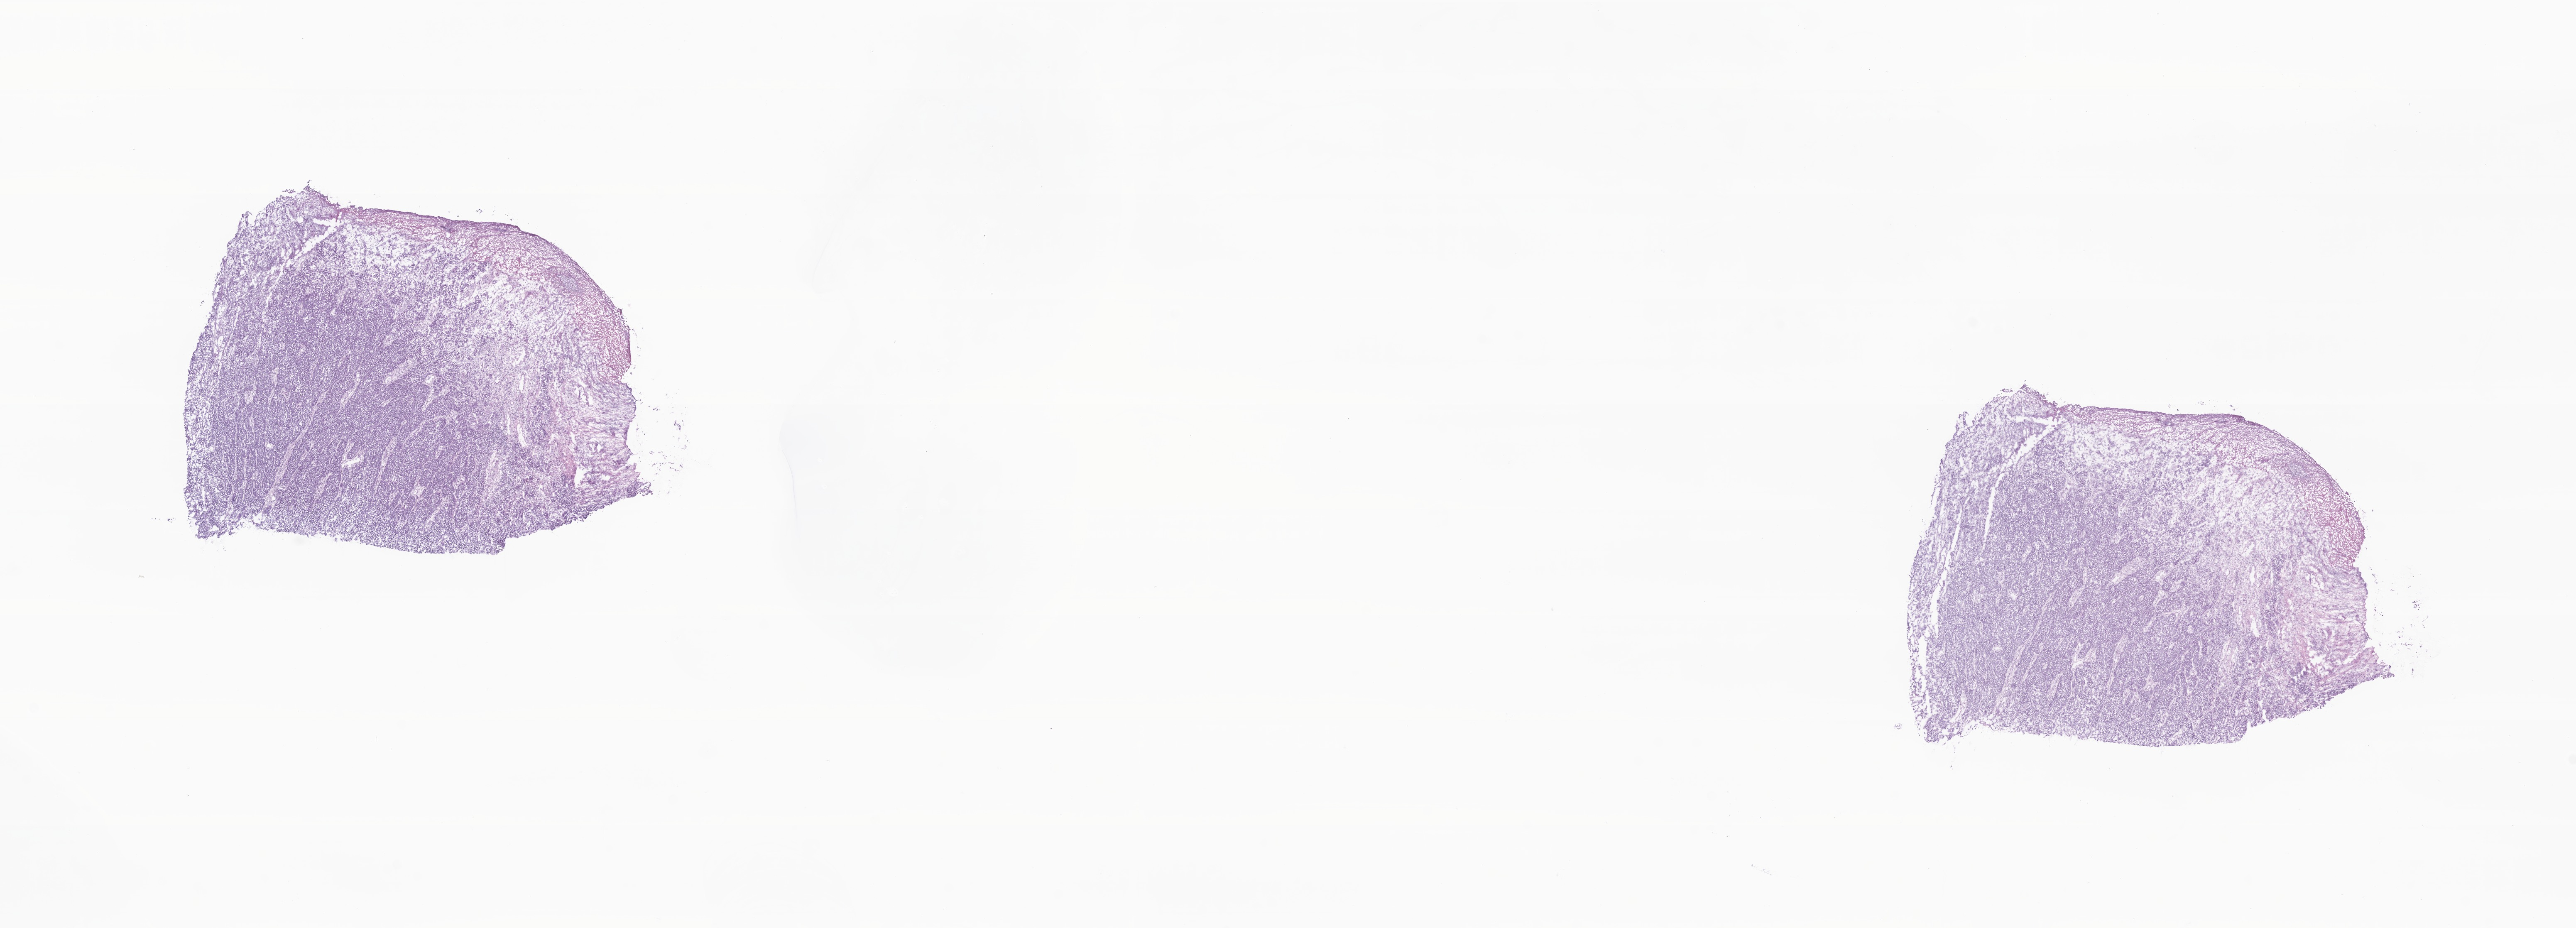
Haematoxylin and eosin whole-slide image — low-resolution overview of the scanned area, about 26.2 x 9.4 mm. Frozen section. Primary tumor. Site: skin. Male, age 66 years at initial diagnosis. Pathologist review of this section (percent, as recorded): tumor cells 80%, tumor nuclei 90%, stromal cells 20%, necrosis 0%, normal cells 0%. Infiltration values recorded for this section: lymphocyte infiltration 0%, monocyte infiltration 0%, neutrophil infiltration 0%.
AJCC pathologic stage: Stage IIIC. Section: top of the tissue portion. Histologic diagnosis: Nodular melanoma.